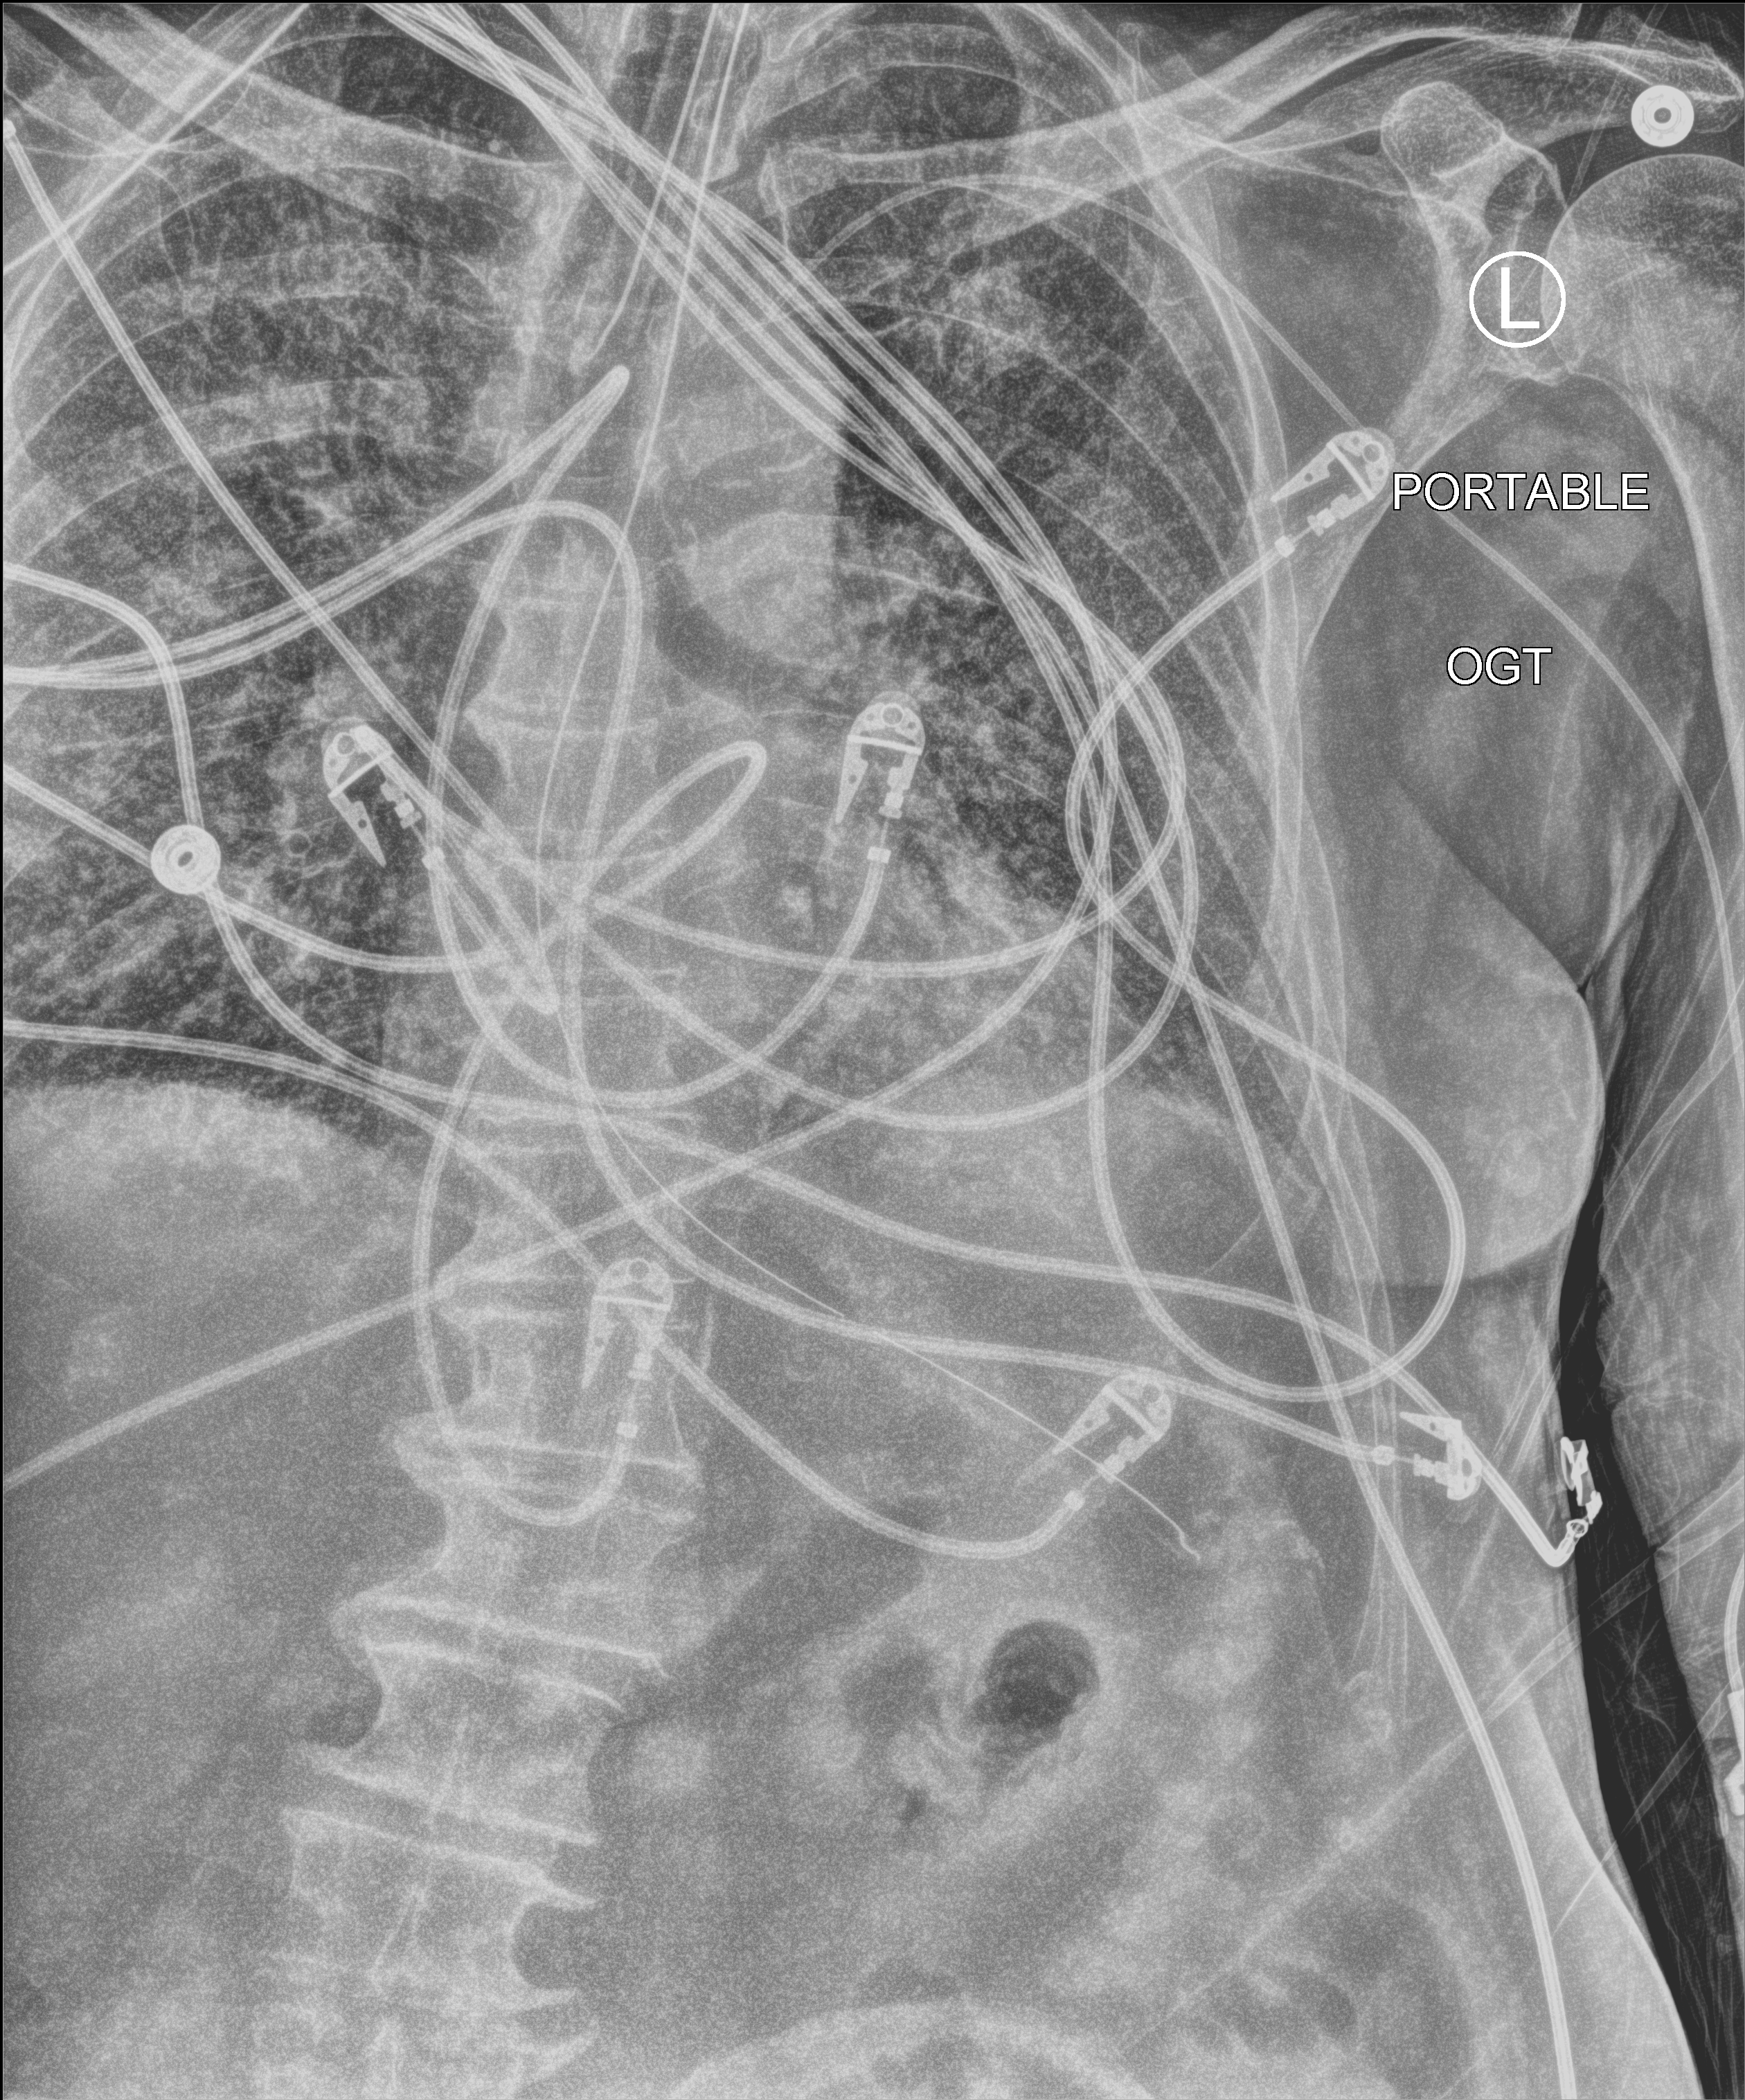
Chest X-ray (portable); anteroposterior (AP) projection. Patient hospitalised with COVID-19; male, aged 75–90 years.
Hospital-stay facts (about this admission, not read from this image; timing relative to this image not recorded):
- admitted to intensive care during this hospital stay: yes